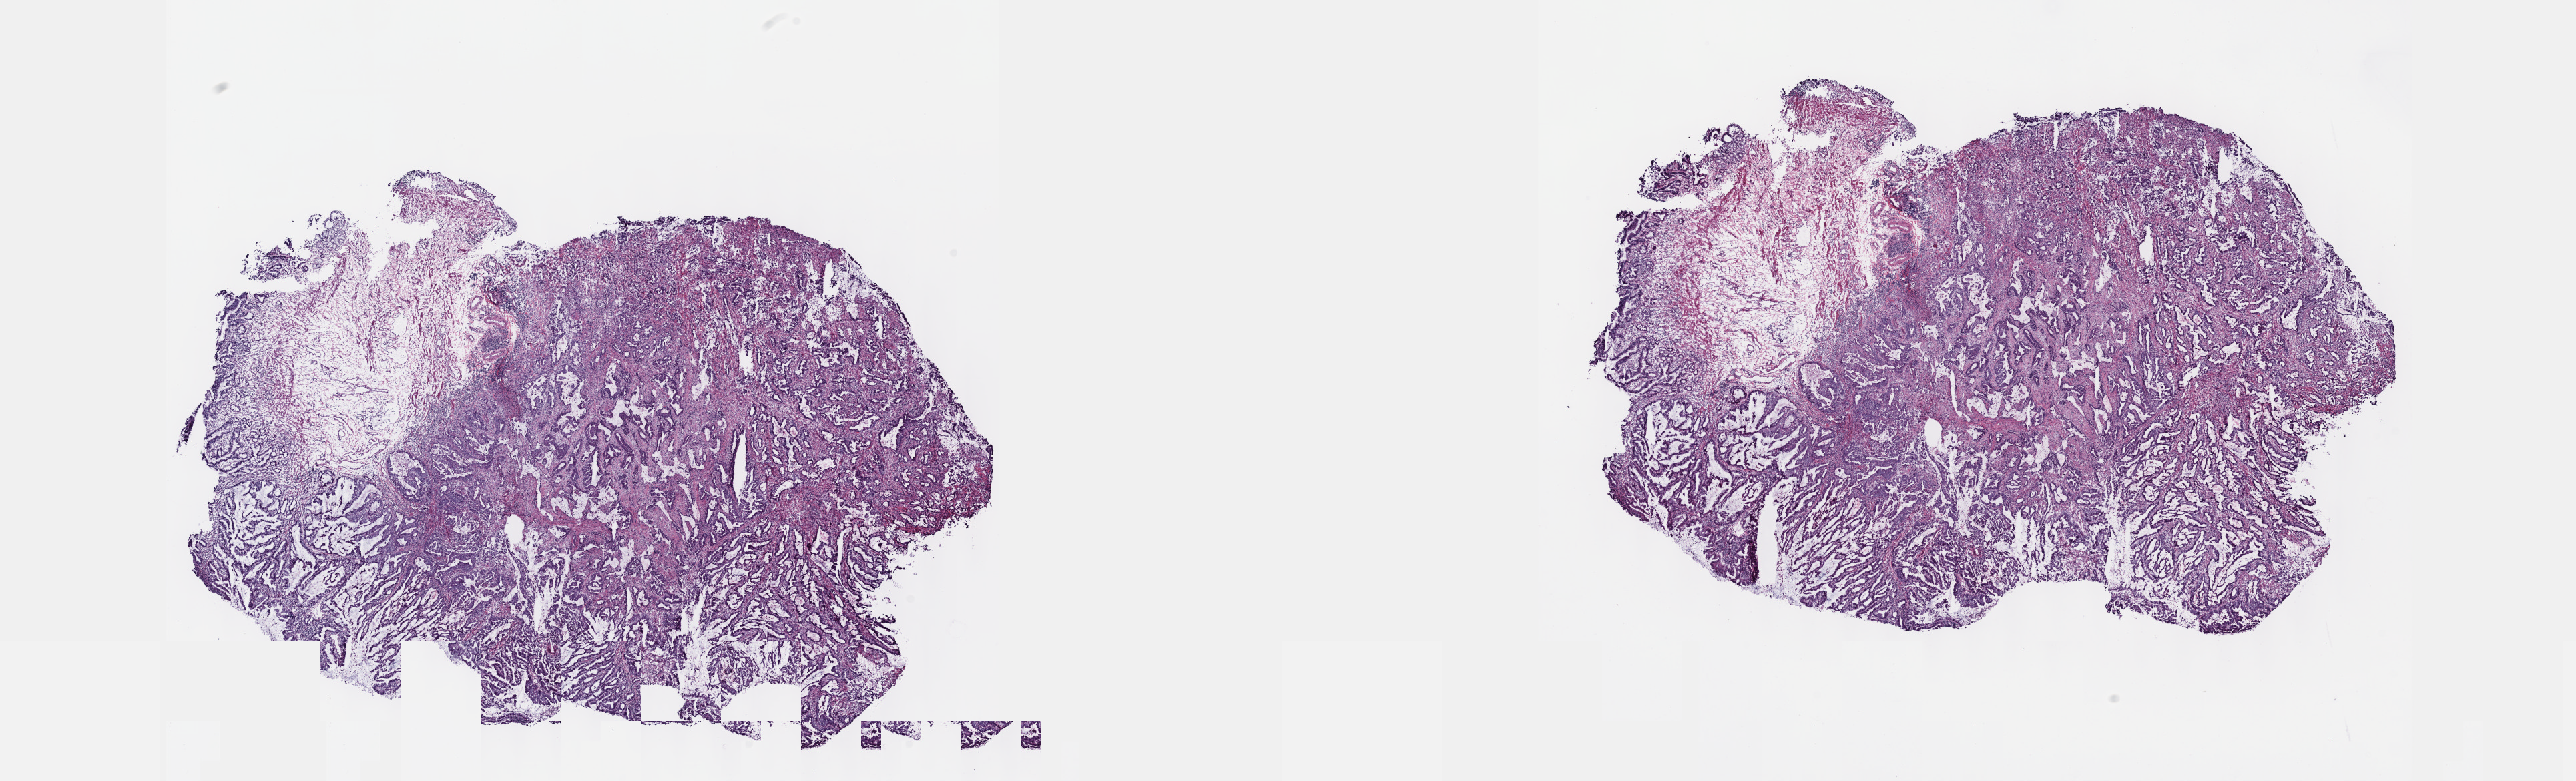
Digitized H&E-stained tissue section (whole slide), shown as a low-resolution overview of the whole scanned area (about 31.2 x 9.5 mm); frozen section; sample: primary tumour, esophagus. Male patient; age at initial diagnosis 44 years. Histologic grade: G2 (moderately differentiated). Slide review estimates, as recorded: tumour cells 70%, tumour nuclei 70%, normal cells 0%, stromal cells 20%, necrosis 10%. Inflammatory infiltration, as recorded: lymphocyte infiltration 40%, monocyte infiltration 20%, neutrophil infiltration 20%.
- lymph nodes positive (case pathology): 1 of 30 examined
- diagnosis: Adenocarcinoma, NOS (lower third of esophagus)
- AJCC pathologic stage: IIB (5th edition)